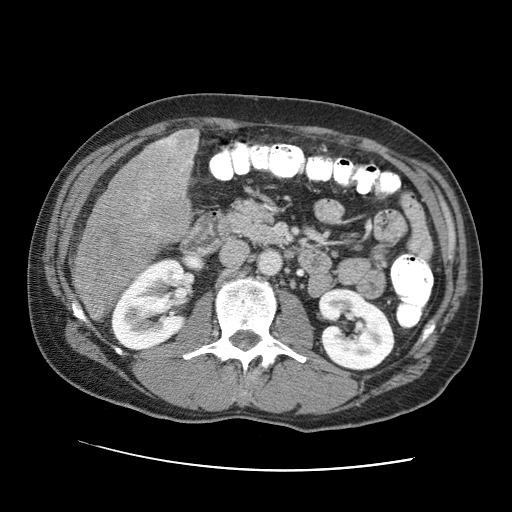
Contrast-enhanced abdominal CT (liver protocol), one axial slice. Slice 24 of 95 in the series (ordered by position). Reconstruction kernel STANDARD. One of 2 acquisitions stored at this slice position. Soft-tissue window (W 400 / L 40 HU). 2.5 mm slice thickness. 512 × 512 image matrix, field of view 360 × 360 mm. From the clinical record (not read from this slice): diagnosis: hepatocellular carcinoma (patient treated with transarterial chemoembolisation; whether this scan precedes or follows treatment is not stated here); TNM stage (as recorded): Stage-IVA; Child-Pugh class: A; tumour differentiation: moderately differentiated; tumour nodularity: multinodular.
Outlined on this slice (semi-automatically segmented with operator editing):
- liver parenchyma outside the tumour (the mass and vessels are separate outlines, so this box may not span the whole liver): bounding box <72,129,198,270> (left, top, right, bottom; pixels)
- mass: <71,128,197,323>